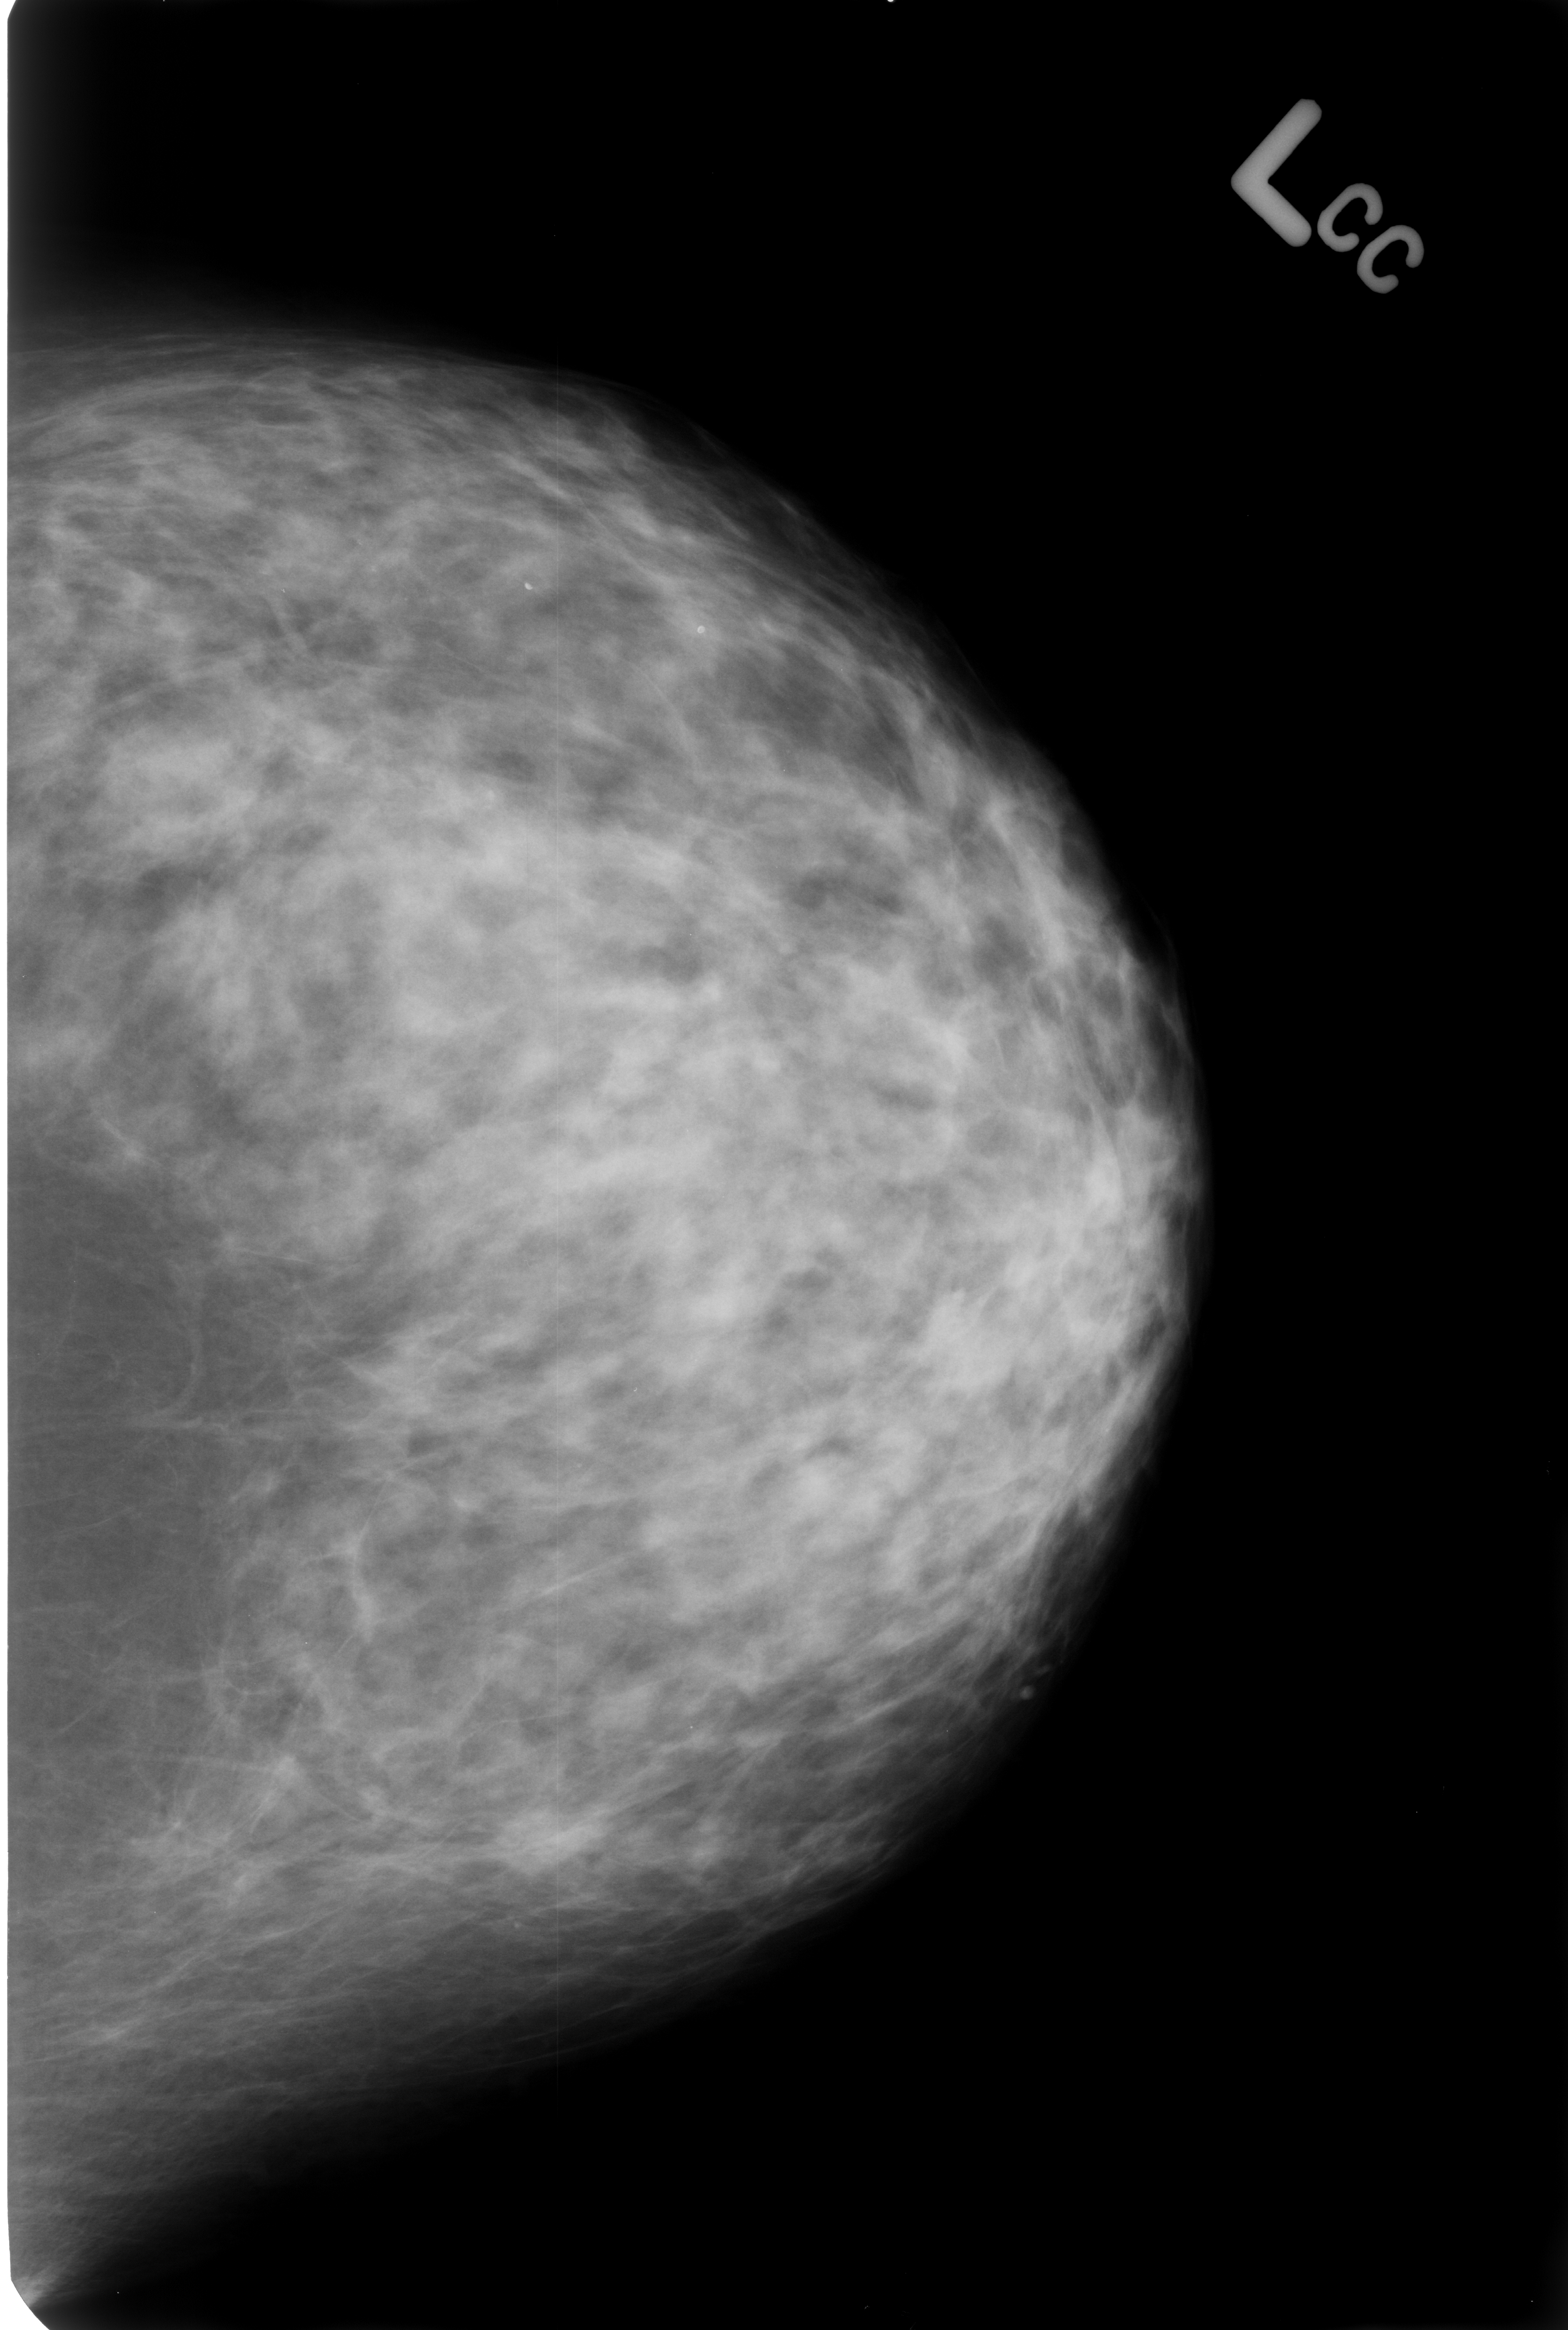
Scanned film-screen mammogram; left breast; craniocaudal (CC) view; breast composition: heterogeneously dense (BI-RADS density category 3 of 4).
- Abnormality record for this image: Finding 1 of 2: calcifications, morphology lucent center; BI-RADS assessment category 2; subtlety rating 3 on a 1 (subtle) to 5 (obvious) scale; benign without callback (not worked up further).
- Finding 2 of 2: calcifications, morphology lucent center; BI-RADS assessment category 2; subtlety rating 3 on a 1 (subtle) to 5 (obvious) scale; benign; no additional work-up was recommended (benign without callback).